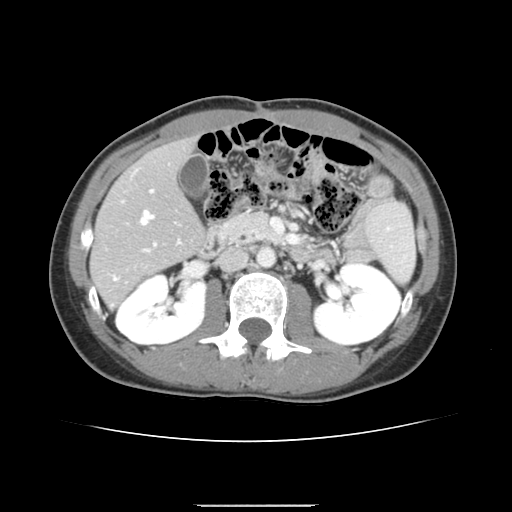
Contrast-enhanced abdominal CT, one axial slice. Slice 68 of 150 in the series (ordered by position). Intravenous contrast given. Soft-tissue window (W 400 / L 40 HU). 2.5 mm slice thickness. 512 × 512 image matrix, field of view 324 × 324 mm. Female patient, age 32 years. From the clinical record (not read from this slice): diagnosis: colorectal cancer liver metastases, imaged before liver resection; multiple liver metastases: yes; largest metastasis: 0.7 cm.
Structures marked on this image (outlined manually by an expert reader):
- hepatic veins: box from (x=114, y=211) to (x=153, y=279) px
- liver: (x=92, y=140)–(x=202, y=305)
- planned liver remnant (the part of the liver to remain after resection): (x=92, y=140)–(x=202, y=289)
- portal vein (with intrahepatic branches): (x=122, y=189)–(x=179, y=252)